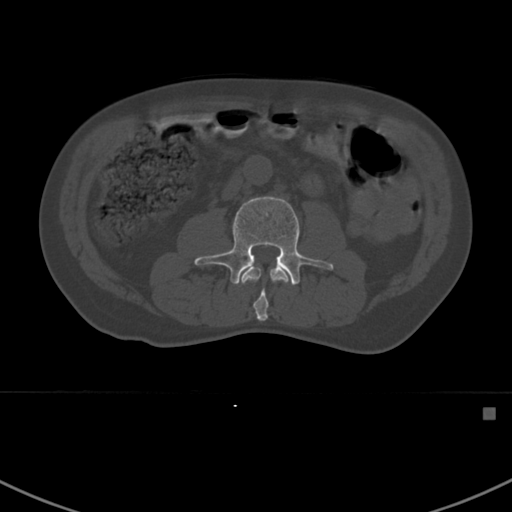
CT including the spine, one axial slice. Slice 270 of 412 in the series (ordered by position). Reconstruction kernel Br40s. 120 kVp. Bone window (W 1800 / L 400 HU). 1.5 mm slice thickness. 512 × 512 image matrix, field of view 358 × 358 mm. Male patient, age 59 years. Case-level facts recorded for this patient, not image findings: primary cancer: prostate.
Structures marked on this image (semi-automatic segmentation, software-assisted and operator-edited):
- L2 vertebra: bounding box [x1, y1, x2, y2] px = [241, 265, 289, 321]
- L3 vertebra: [194, 196, 334, 285]